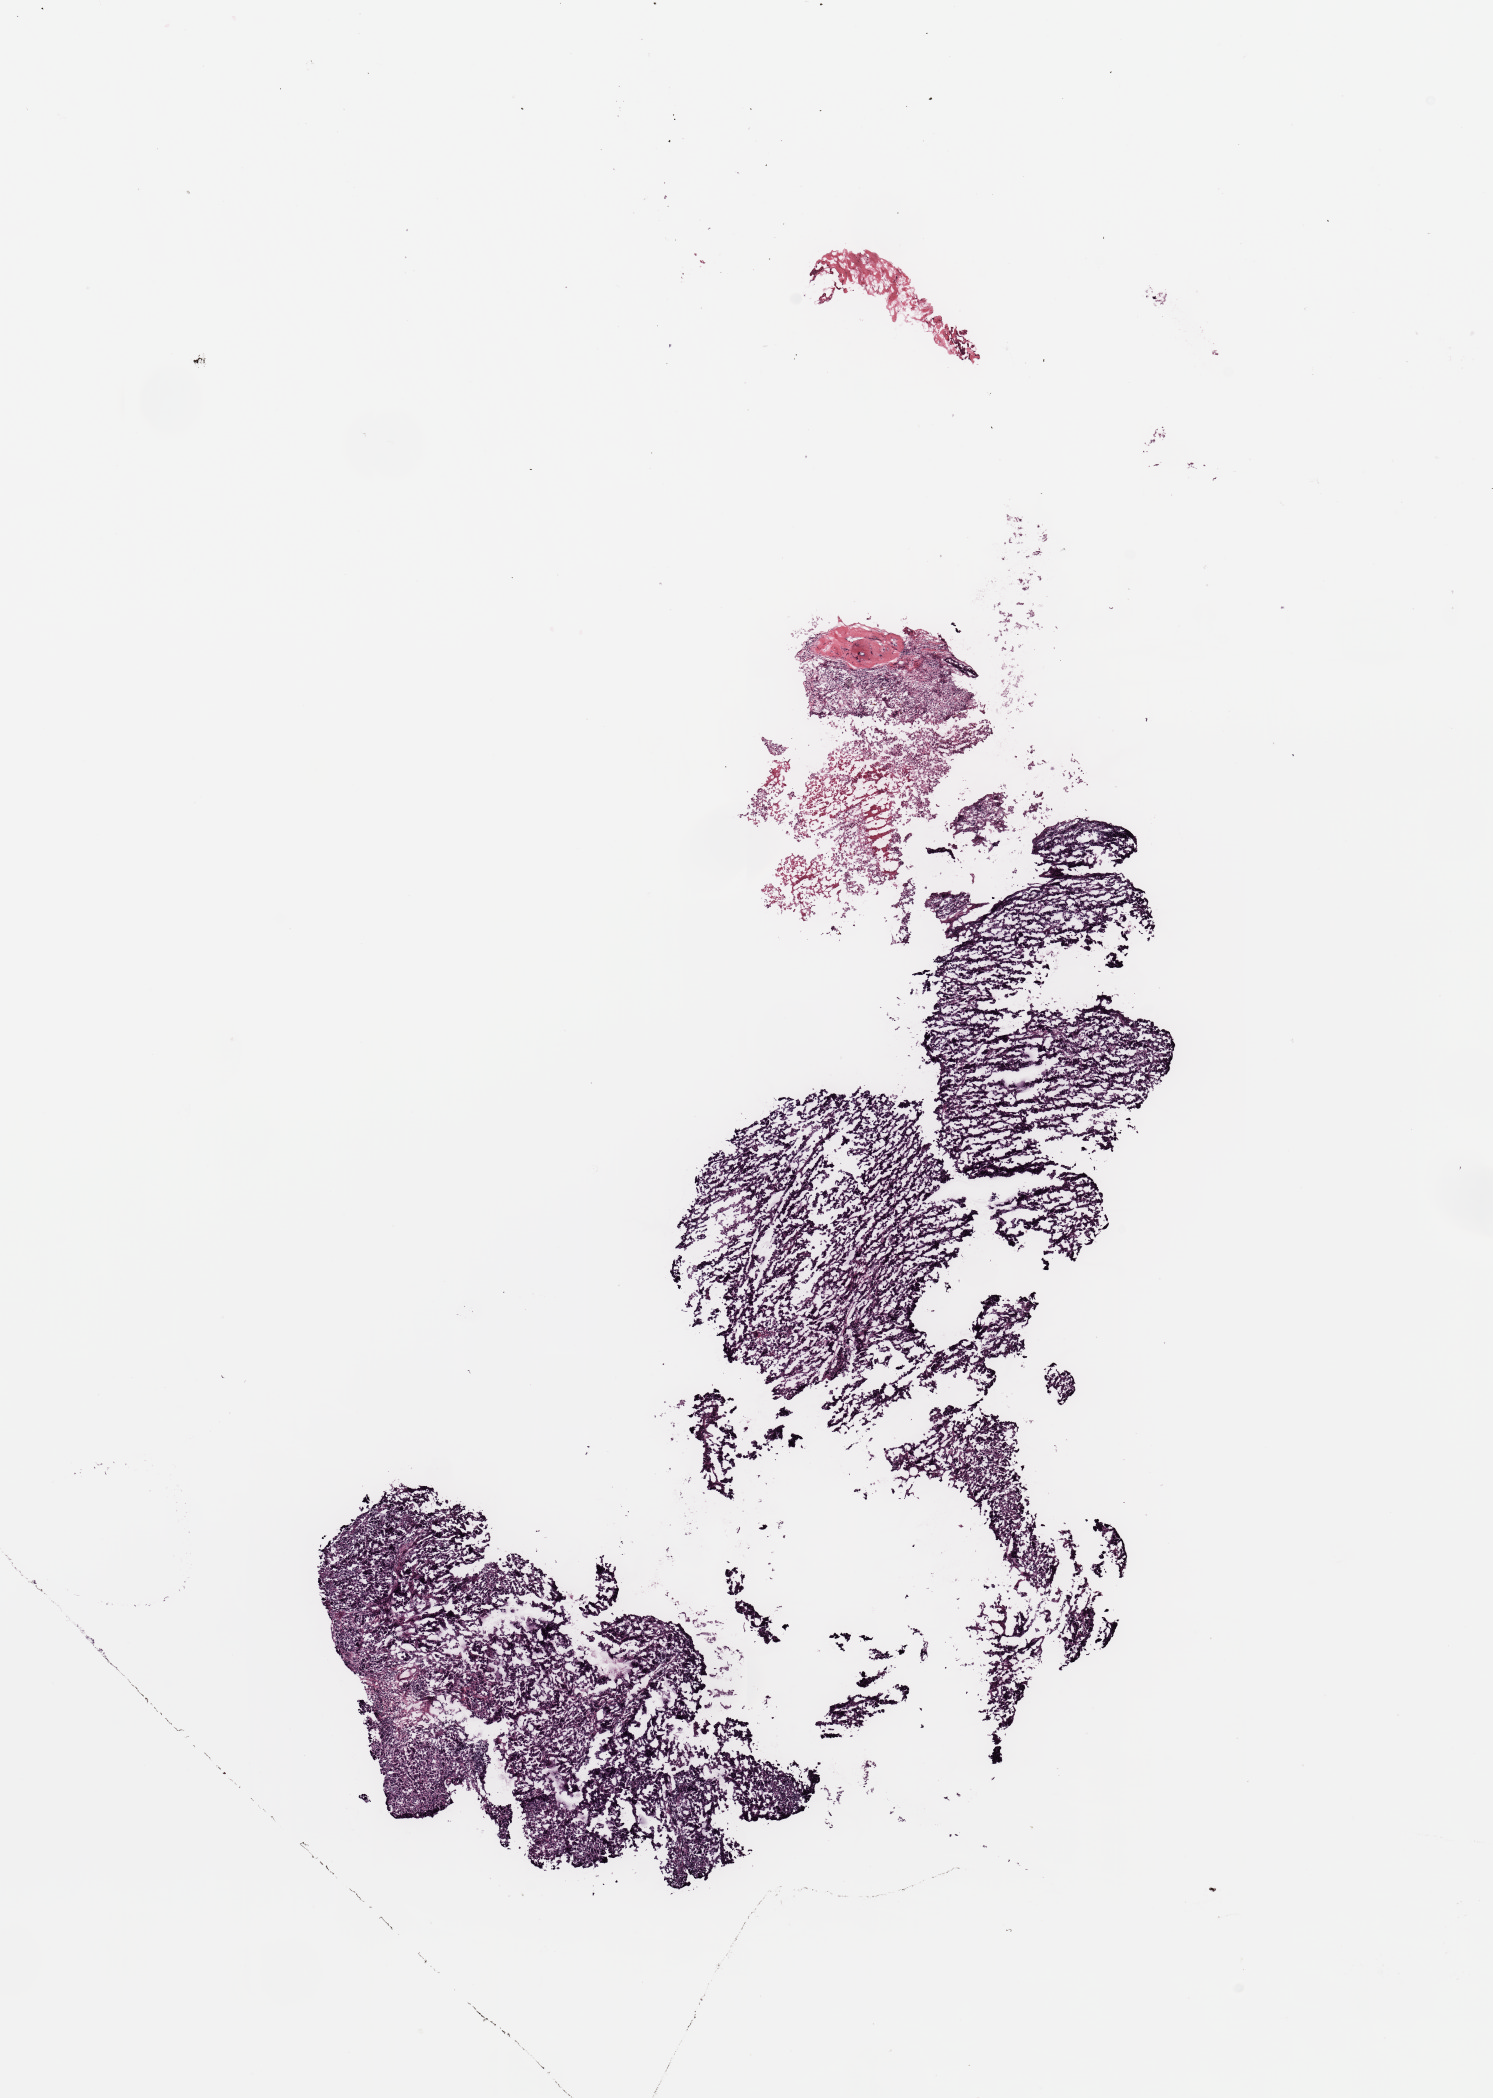
H&E-stained whole-slide image — whole scanned area (about 11.8 x 16.6 mm, slide scanned at 20x) shown as a low-resolution overview, tumour tissue sample, breast. Patient: female, age 58 years.
Histologic diagnosis: Infiltrating duct carcinoma, NOS. AJCC pathologic stage: II.